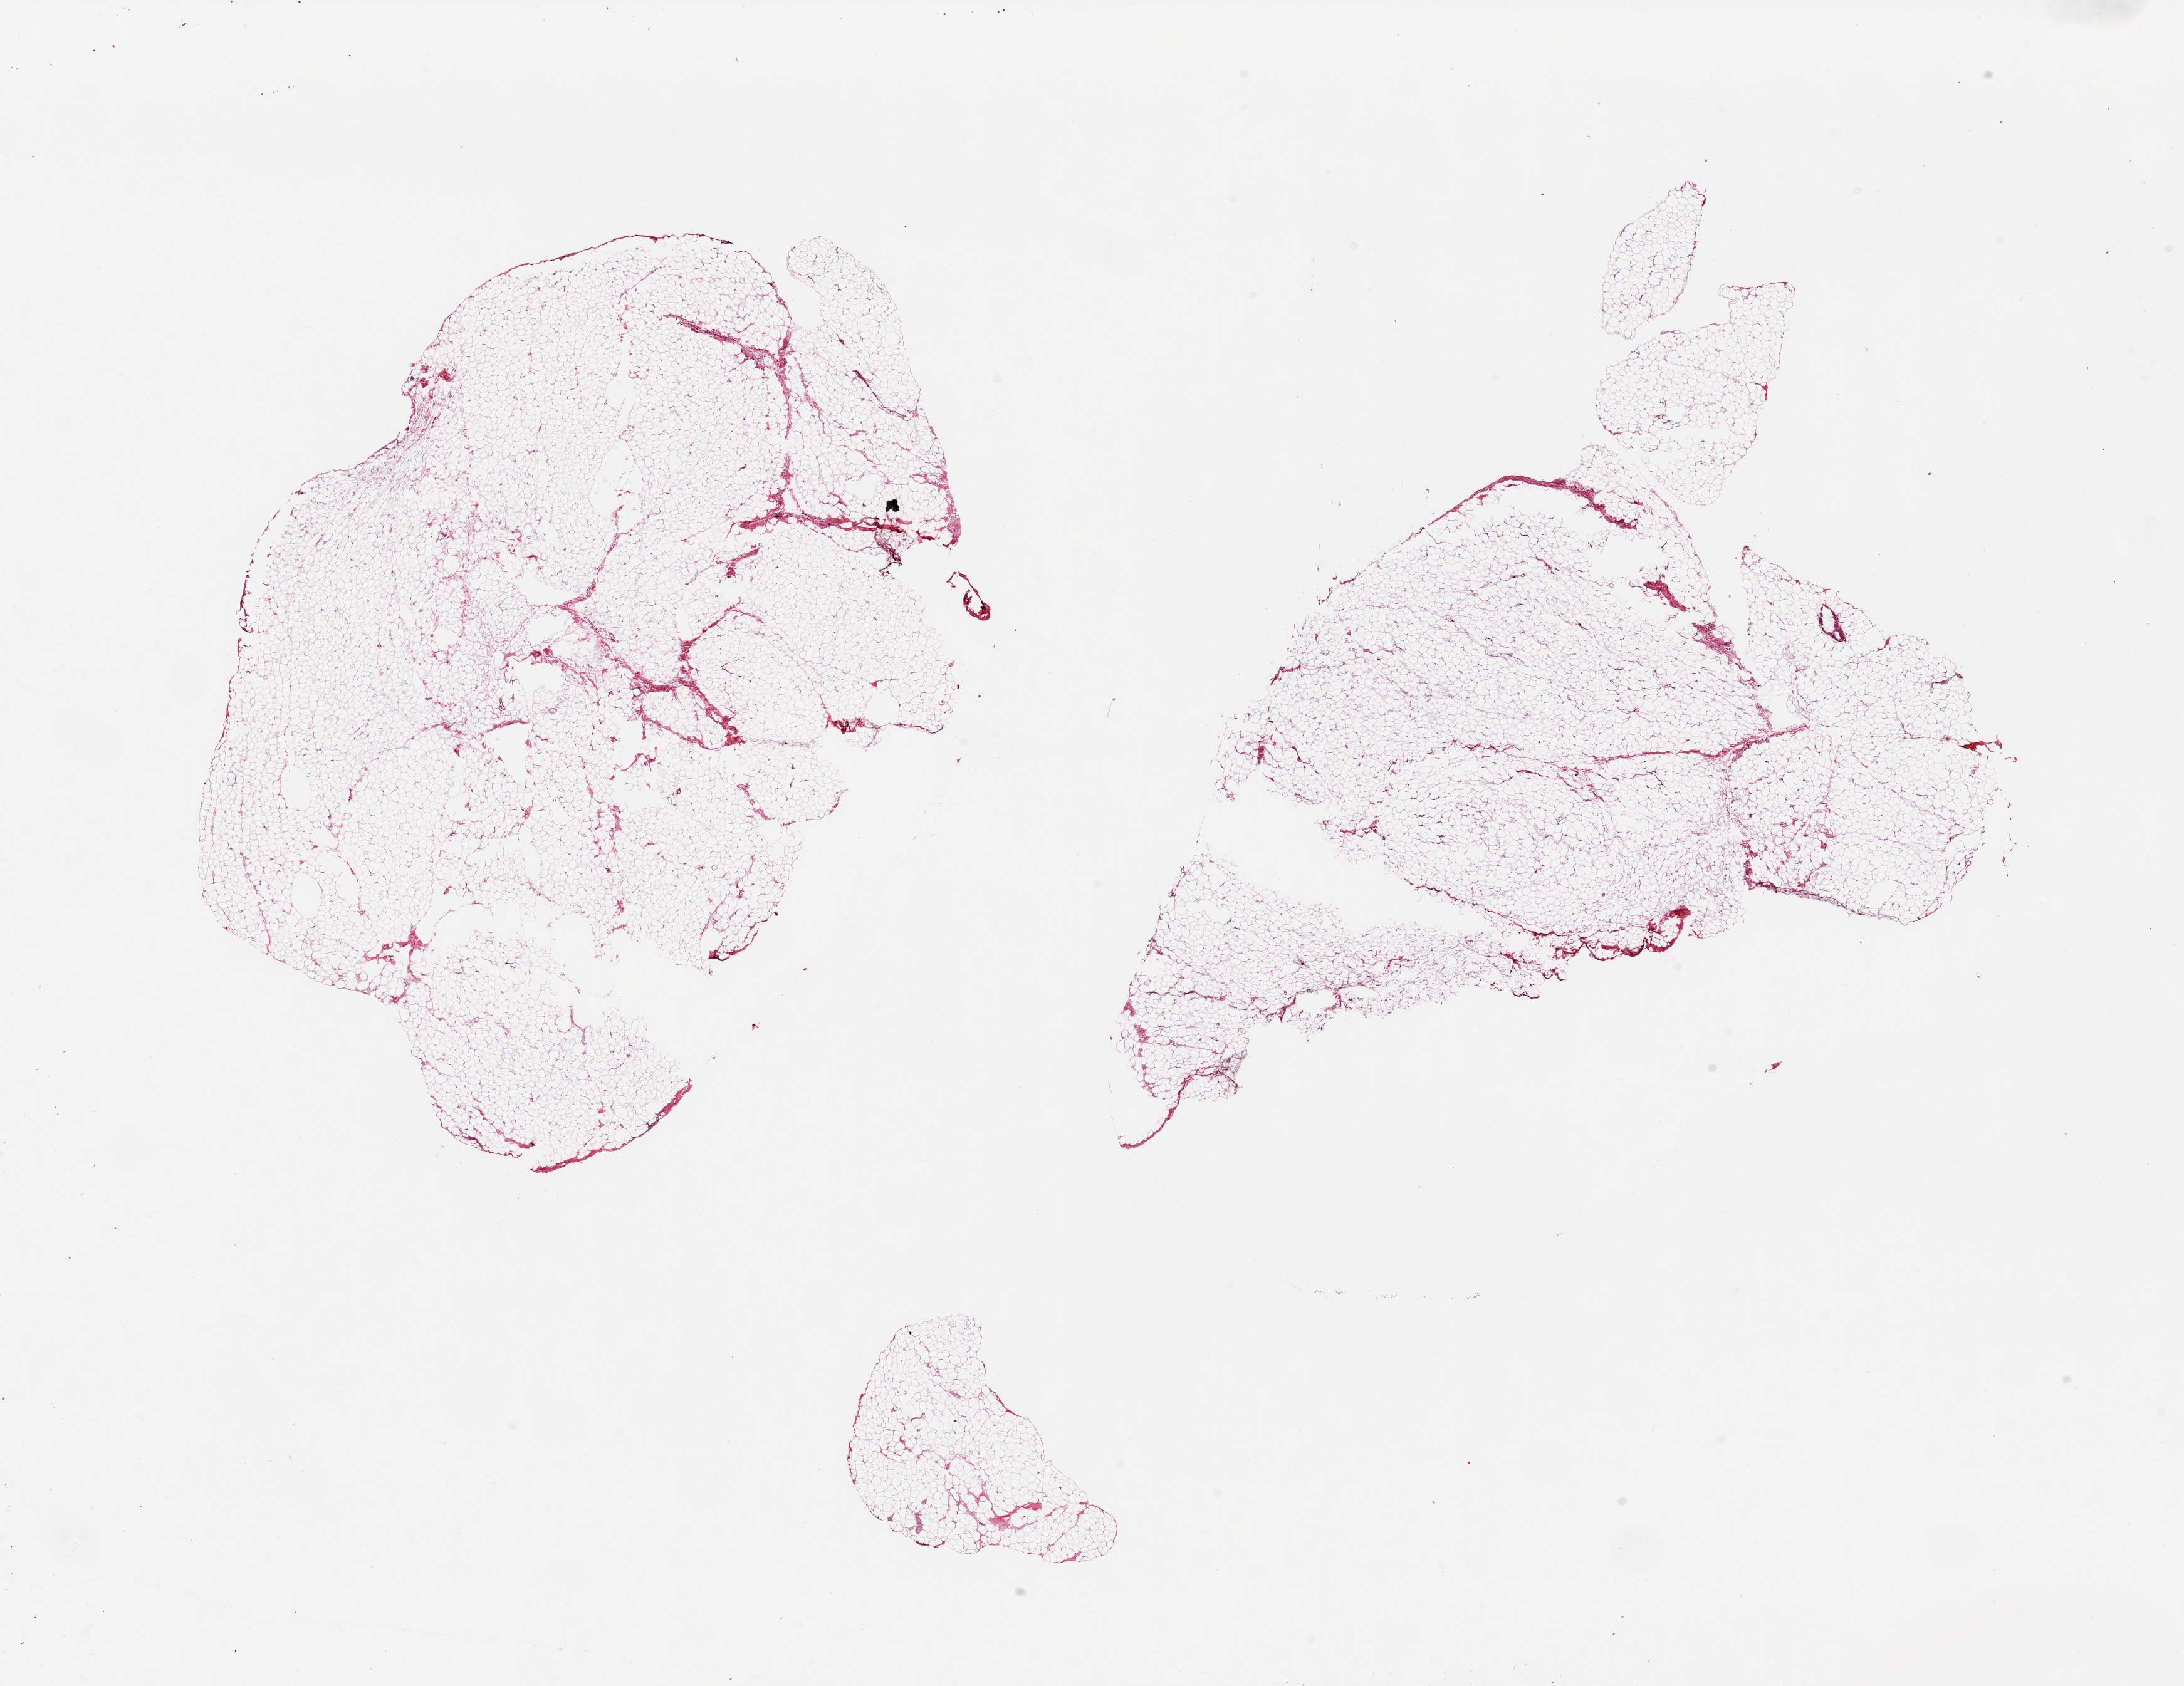
Digitized hematoxylin and eosin (H&E)-stained section — a low-resolution overview of the entire scanned area, about 27.6 x 21.3 mm (slide scanned at 20x). PAXgene-fixed, paraffin-embedded tissue. Section of omentum (target tissue). Tissue donor sample. Donor sex: male.
Pathologist's review note for this sample: 2 pieces; <2% fibrous content.